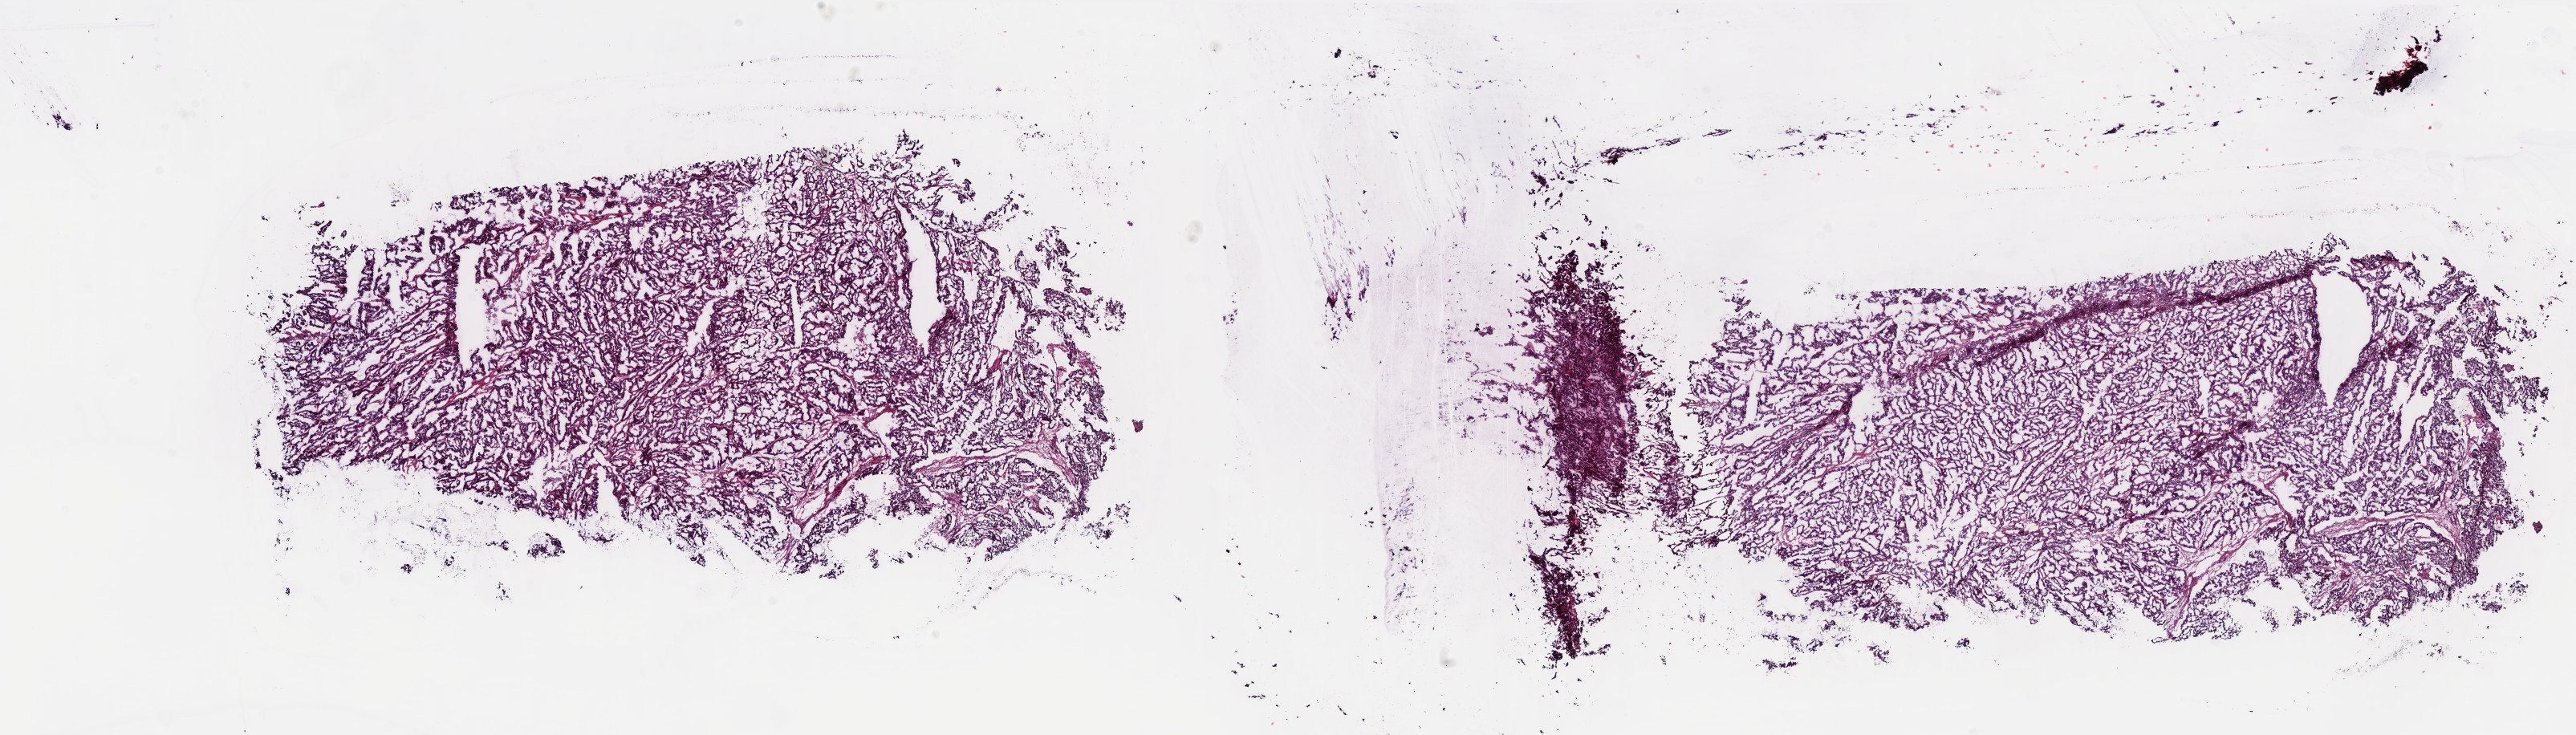
Hematoxylin and eosin (H&E) stained whole-slide image — whole scanned area (about 25.7 x 7.3 mm, slide scanned at 40x) shown as a low-resolution overview; frozen section; uterus, primary tumour sample. Female patient; age at initial diagnosis 81 years. Histologic grade: G3 (poorly differentiated). Slide review estimates, as recorded: tumour cells 93%, tumour nuclei 96%, normal cells 0%, stromal cells 5%, necrosis 2%. Infiltration values recorded for this section: lymphocyte infiltration 0%, monocyte infiltration 0%, neutrophil infiltration 0%.
- FIGO stage: II
- histologic diagnosis: Serous cystadenocarcinoma, NOS